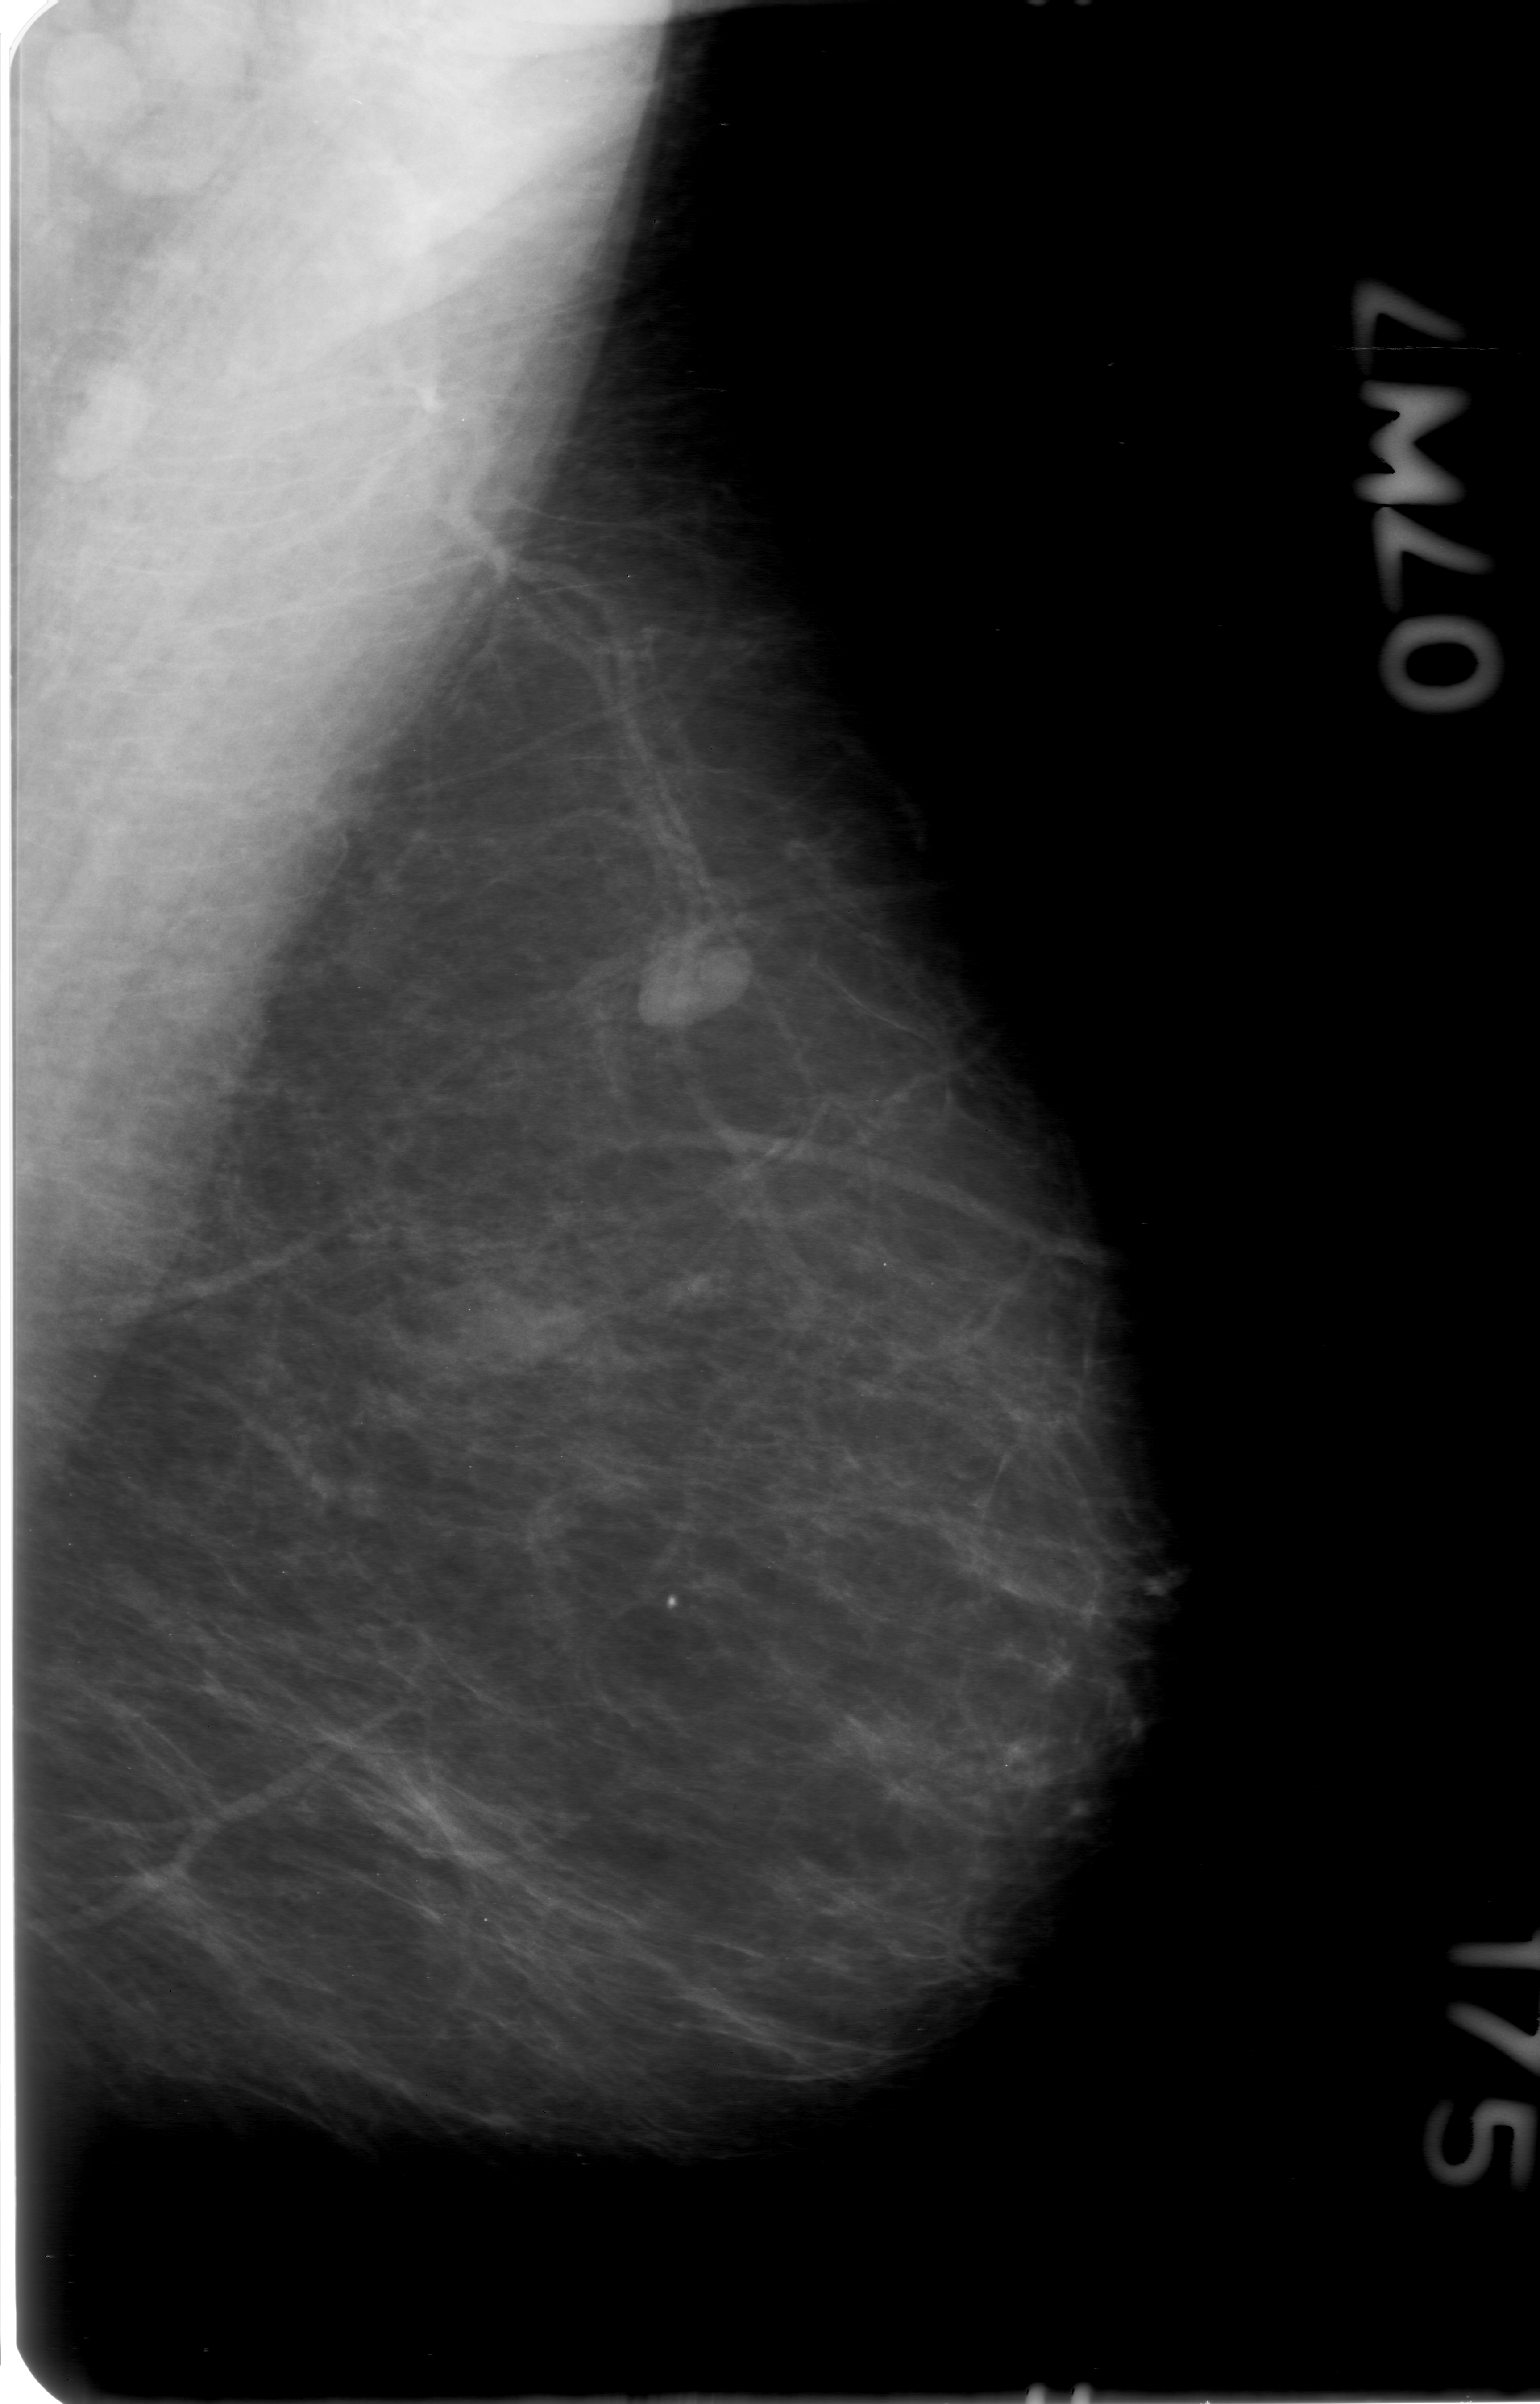
Mammogram (digitized film). Left breast. MLO view. BI-RADS breast density category 1 (scale 1–4). 1540 × 2404 image matrix.
Expert-marked regions of interest on this image (one box per marked abnormality):
- mass, shape lobulated, margins obscured; BI-RADS assessment category 0 (incomplete: needs additional imaging); subtlety rating 4 on a 1 (subtle) to 5 (obvious) scale; pathology result (as recorded, not read from the image): benign: bounding box <466,1247,623,1378> (left, top, right, bottom; pixels)